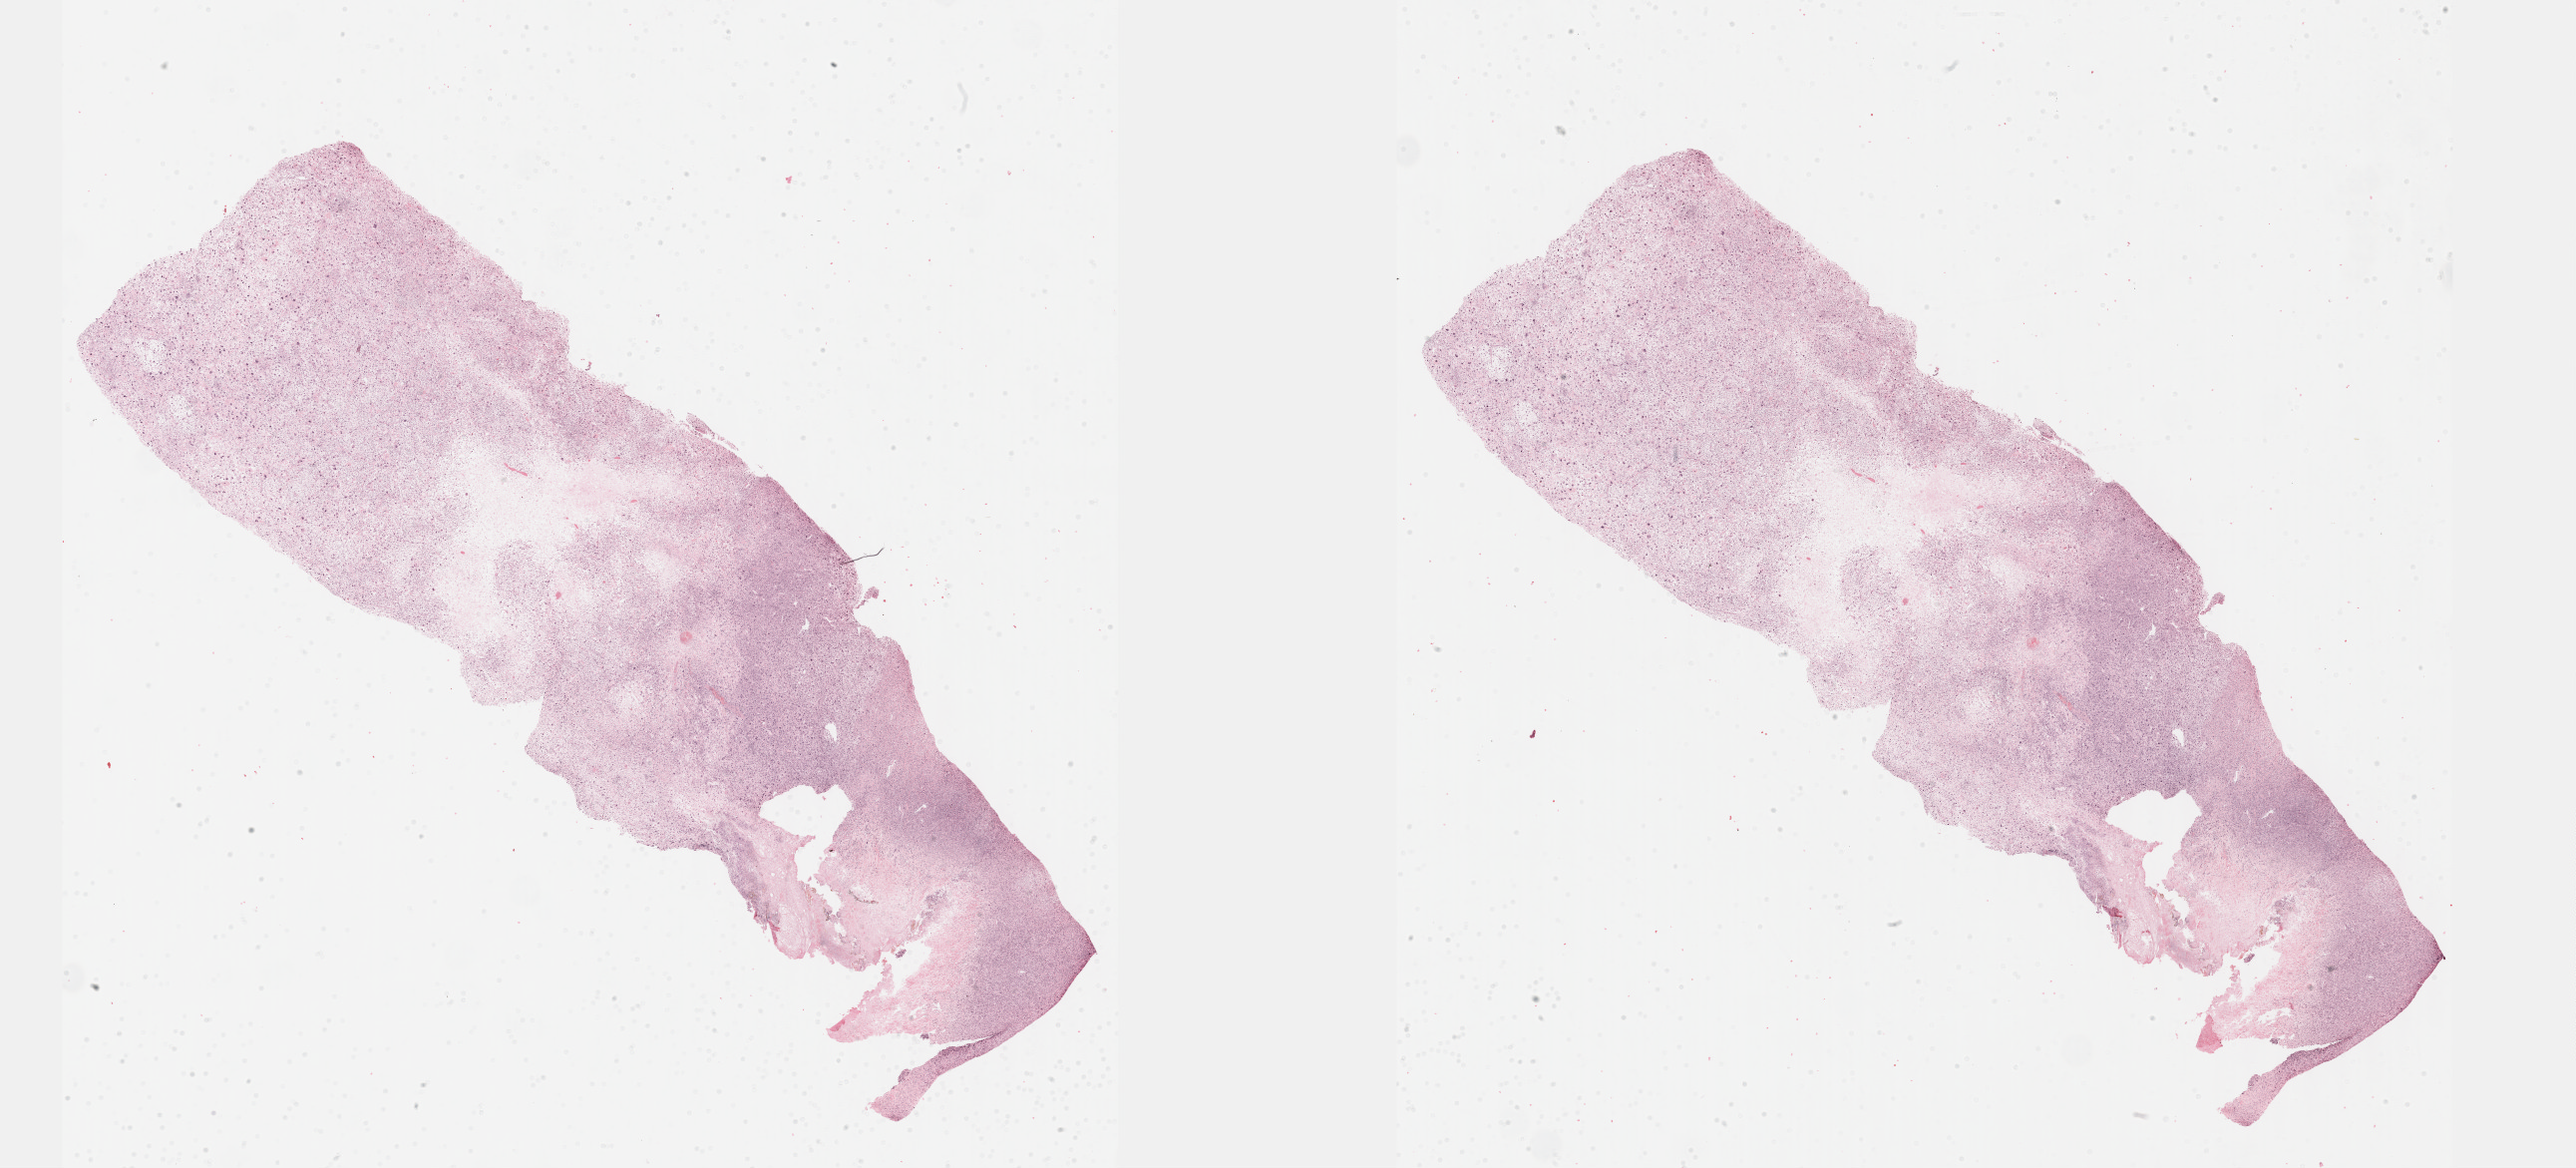
Digitized H&E tissue section (whole slide) — shown as a low-resolution overview of the whole scanned area (about 41.7 x 18.9 mm). Formalin-fixed paraffin-embedded (FFPE) diagnostic section. Sample: primary tumour, connective, subcutaneous and other soft tissues. Patient: male, age at initial diagnosis 49 years.
* pathologic diagnosis: Undifferentiated sarcoma (connective, subcutaneous and other soft tissues of lower limb and hip)